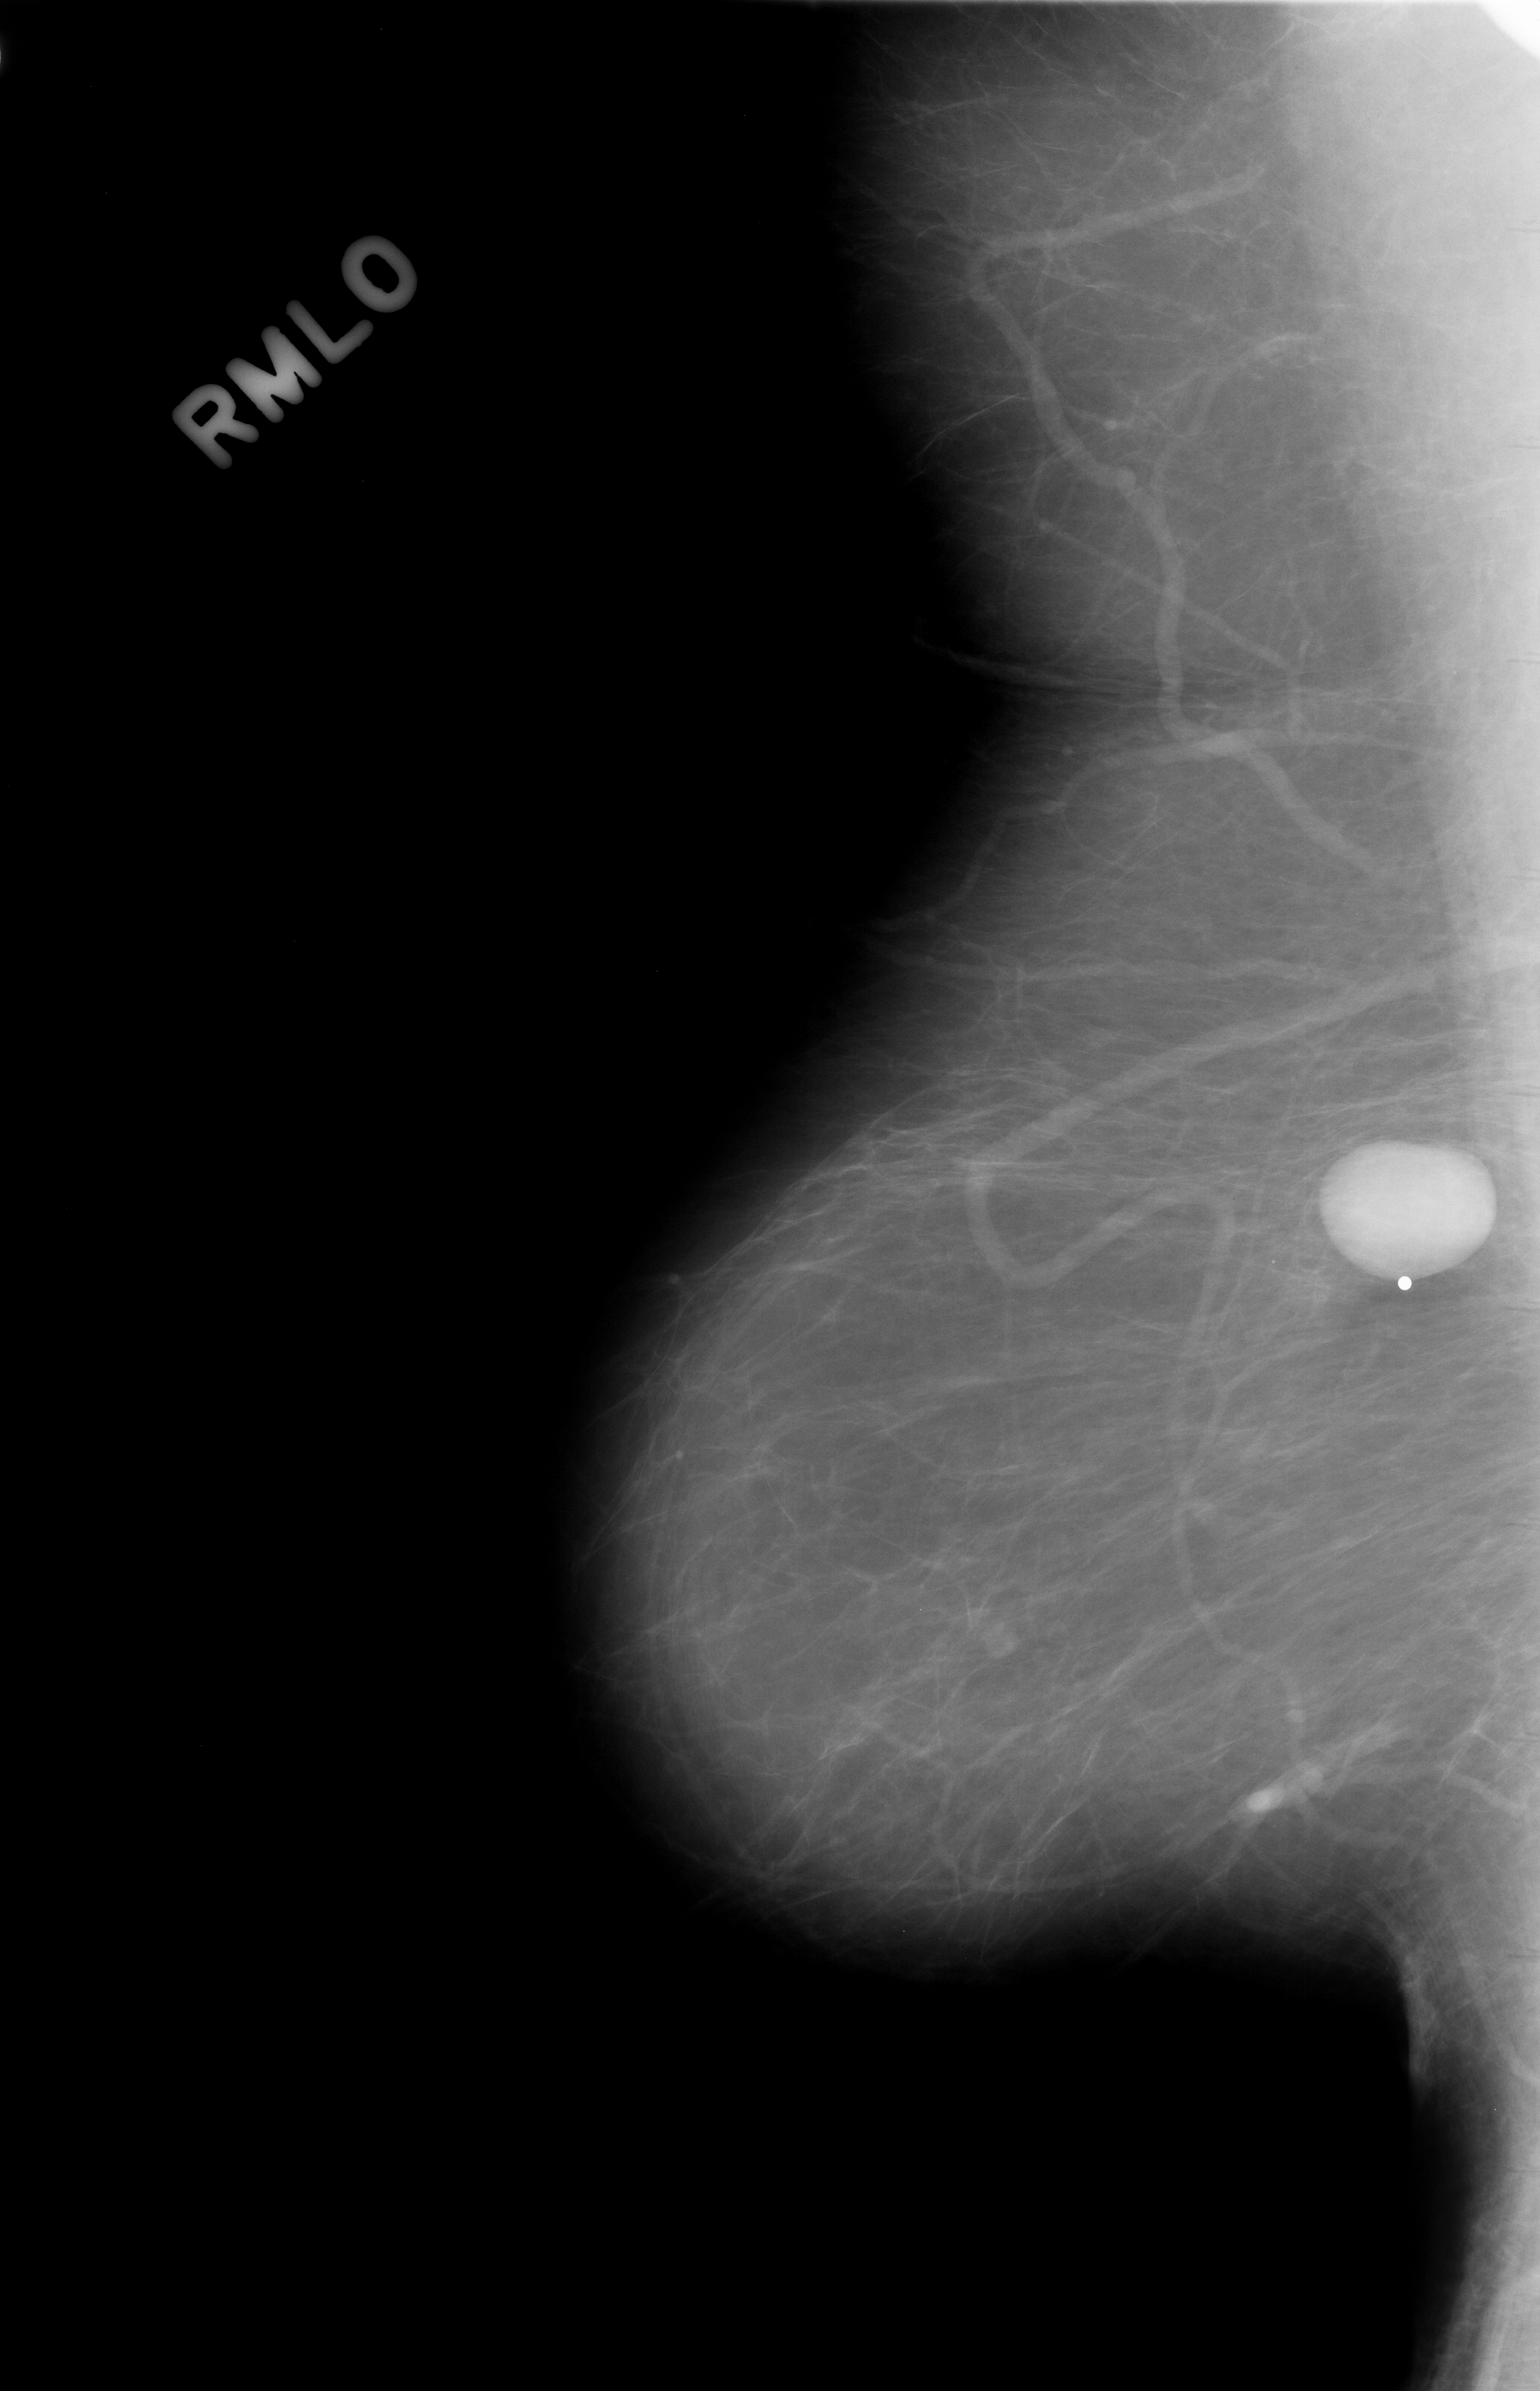
Scanned film-screen mammogram; right breast; mediolateral oblique (MLO) view; BI-RADS breast density category 1 (scale 1–4).
Marked abnormality: mass, shape oval, margins circumscribed; BI-RADS assessment category 4; subtlety rating 5 on a 1 (subtle) to 5 (obvious) scale; pathology (as recorded): benign.